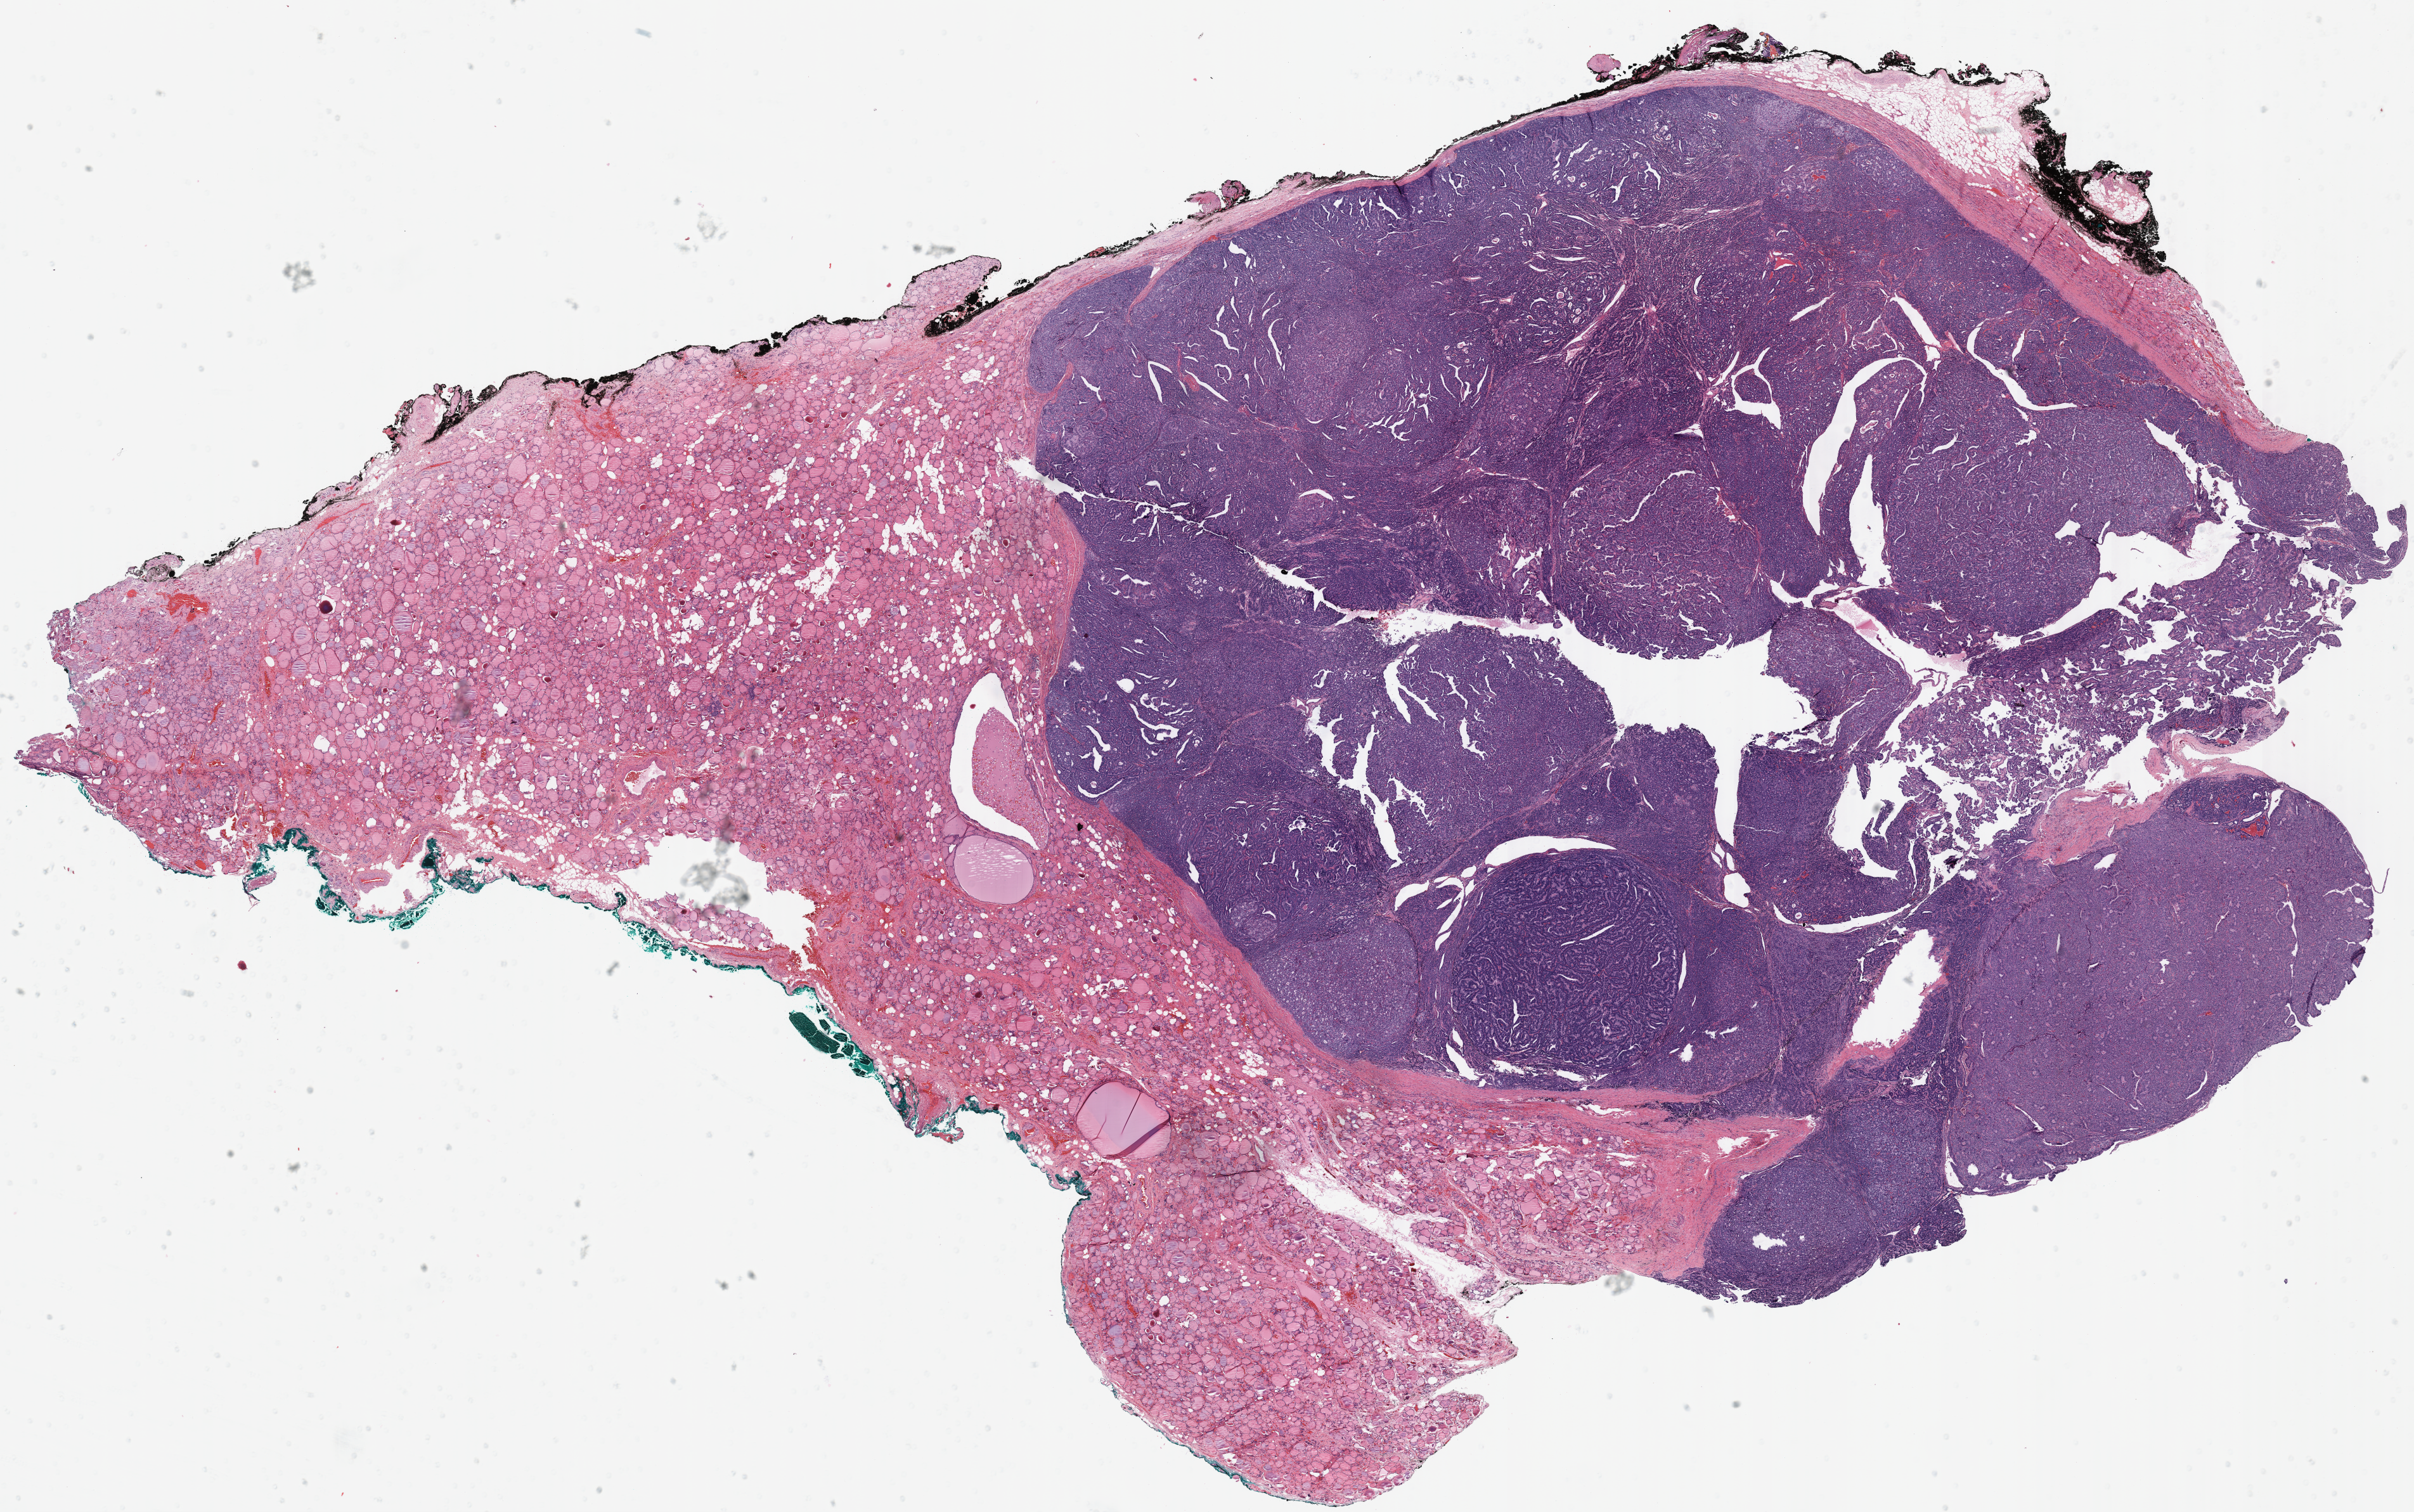
Digitized Hematoxylin and eosin (H&E) stained tissue section (whole slide), shown as a low-resolution overview of the whole scanned area (about 30.0 x 18.8 mm, from a 40x scan). Formalin-fixed paraffin-embedded (FFPE) diagnostic section. Primary tumour sample from the thyroid. Female patient; age at initial diagnosis 51 years.
Diagnosis: Papillary adenocarcinoma, NOS (thyroid gland).